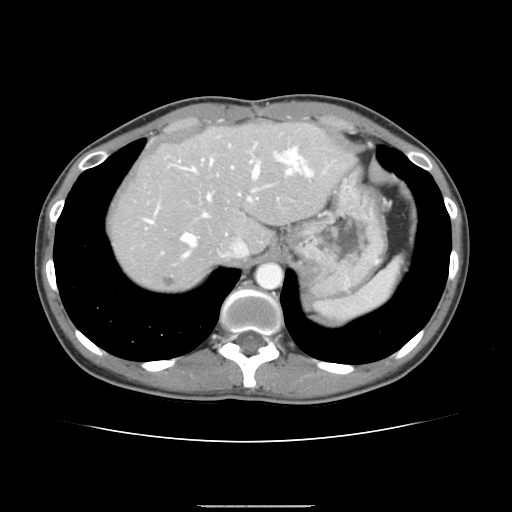
Contrast-enhanced abdominal CT, one axial slice; position 117 of 150 along the scan axis; 120 kVp; intravenous contrast given; soft-tissue window (W 400 / L 40 HU); 2.5 mm slice thickness; 512 × 512 image matrix. Female patient, age 32 years. From the clinical record (not read from this slice): diagnosis: colorectal cancer liver metastases, imaged before liver resection; multiple liver metastases: yes; largest metastasis: 0.7 cm; disease in both lobes: no.
Annotated regions visible in this slice (manually delineated by an expert):
- hepatic veins: bounding box (x1, y1, x2, y2) in pixels: (145, 151, 296, 259)
- liver: (110, 123, 350, 291)
- planned liver remnant (the part of the liver to remain after resection): (110, 124, 351, 261)
- portal vein (with intrahepatic branches): (179, 148, 313, 216)
- liver metastasis: (161, 276, 175, 287)